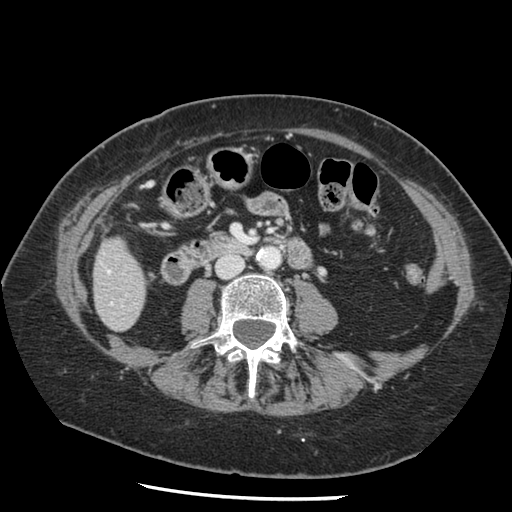
Contrast-enhanced abdominal CT, one axial slice; position 27 of 148 along the scan axis; intravenous contrast given; soft-tissue window (W 400 / L 40 HU); 2.5 mm slice thickness; 512 × 512 image matrix. Female patient, age 85 years. From the clinical record (not read from this slice): diagnosis: colorectal cancer liver metastases, imaged before liver resection; multiple liver metastases: no; largest metastasis: 0.9 cm; disease in both lobes: no.
Structures marked on this image (manually delineated by an expert):
- liver: bounding box (x1, y1, x2, y2) in pixels: (94, 239, 146, 331)
- planned liver remnant (the part of the liver to remain after resection): (94, 239, 146, 331)